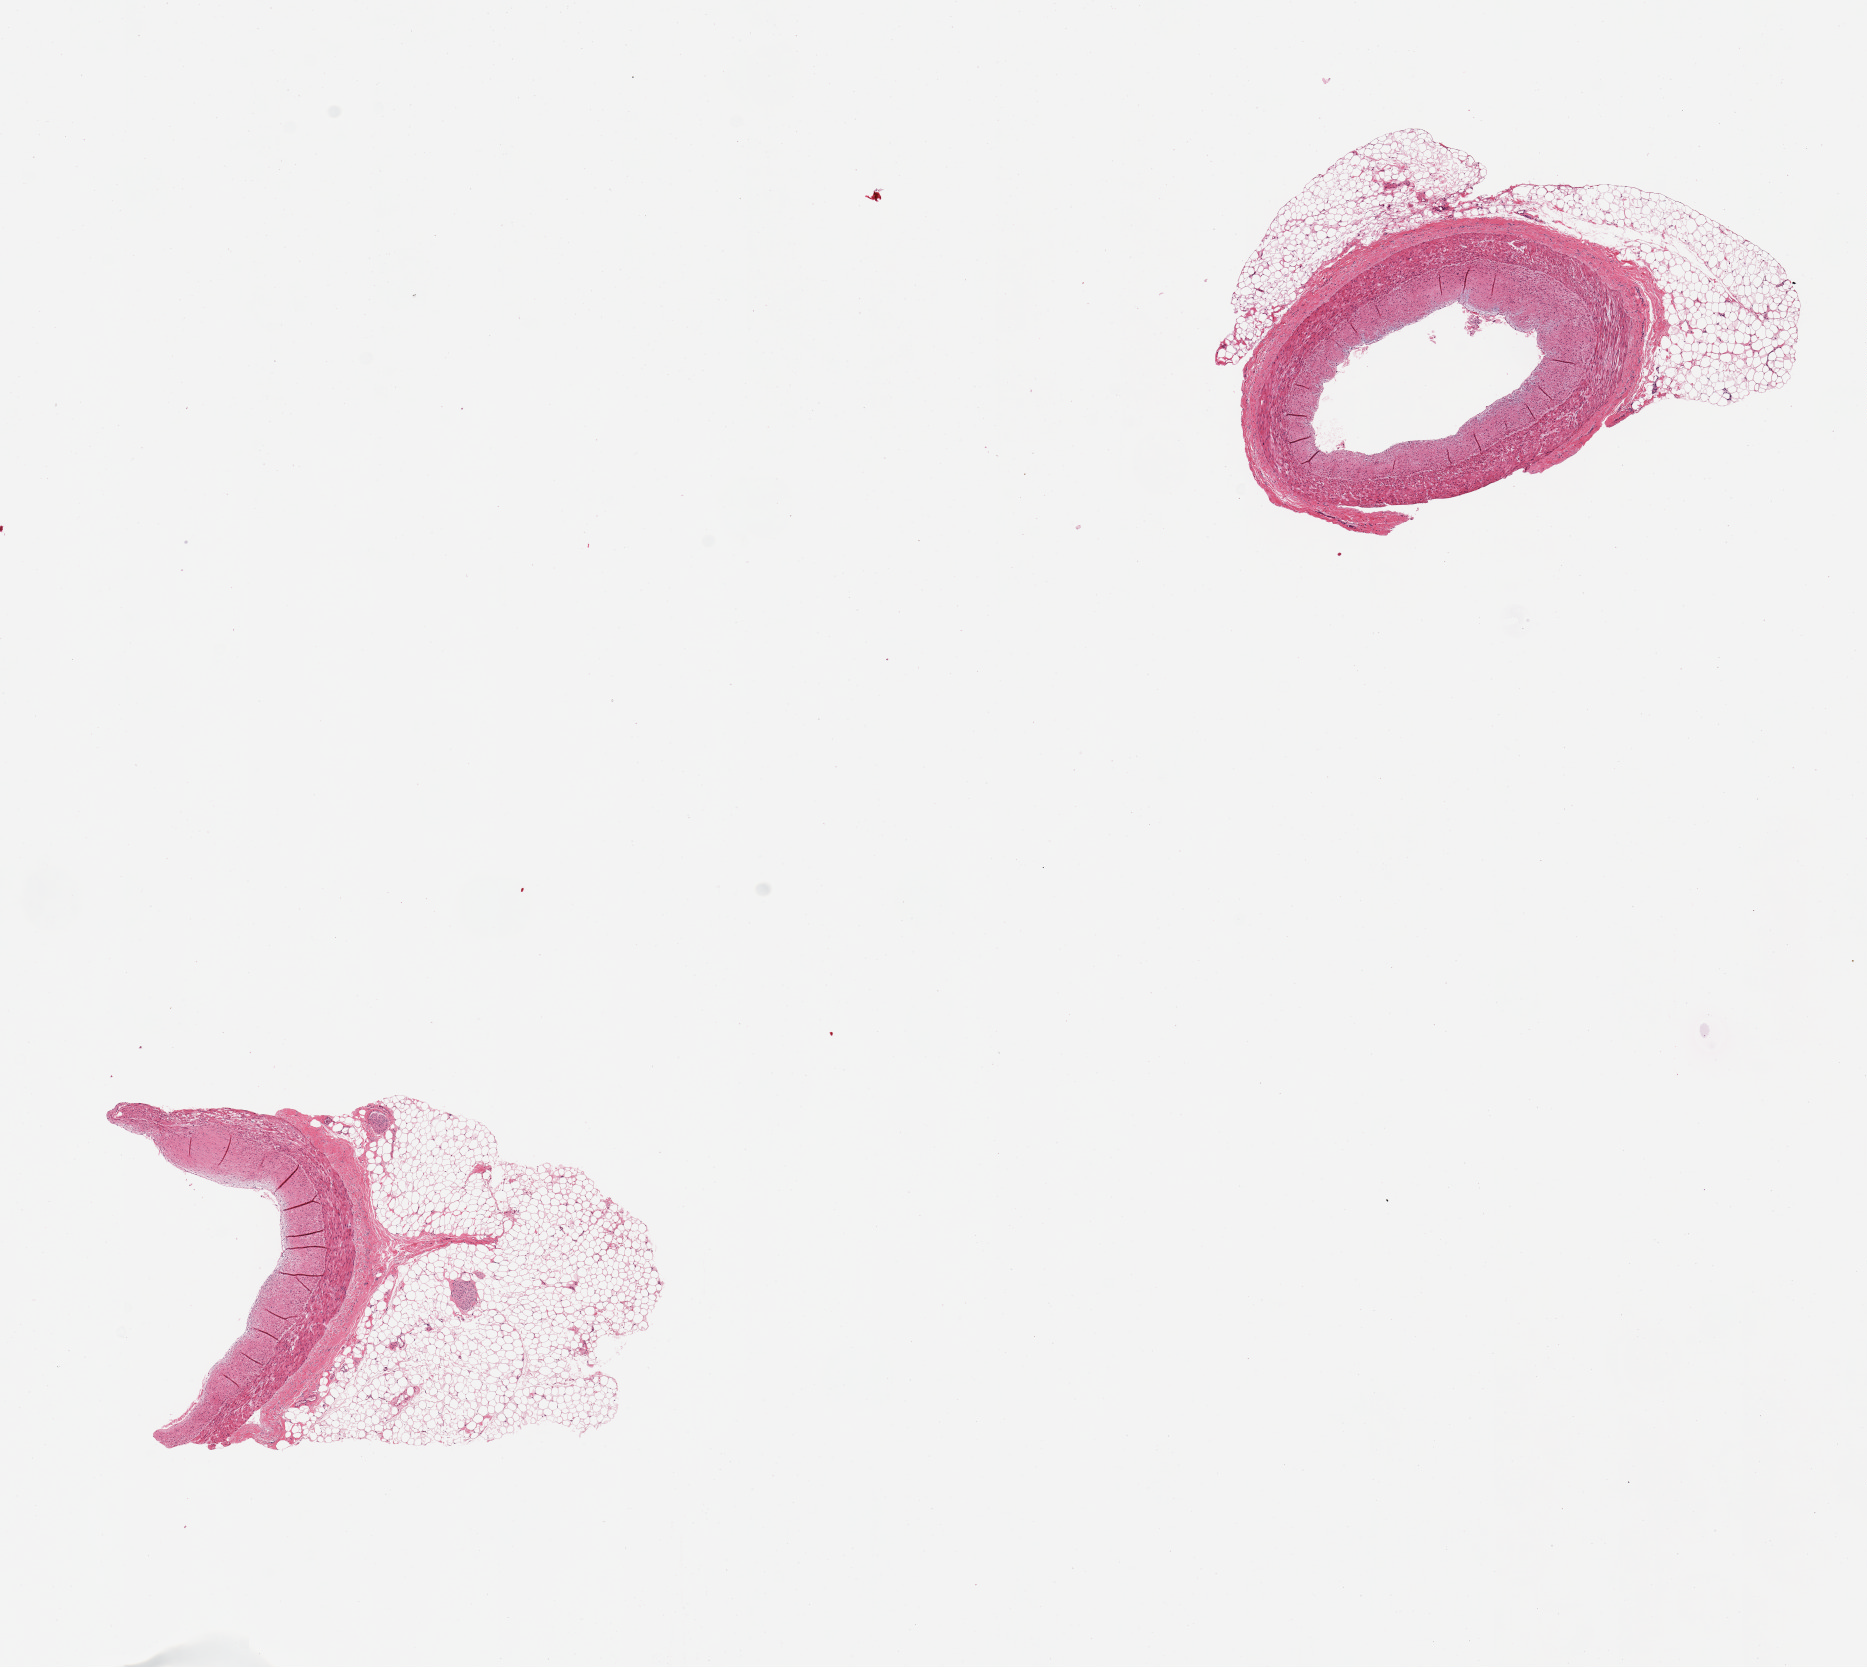
Whole-slide image, haematoxylin and eosin stain, brightfield — a low-resolution overview of the entire scanned area, about 14.8 x 13.2 mm; PAXgene-fixed, paraffin-embedded tissue; section of coronary artery (target tissue); donor tissue sample.
Reviewer comment on this tissue sample: 2 pieces; 1 with 60% fat, other with 40% fat; not well trimmed.